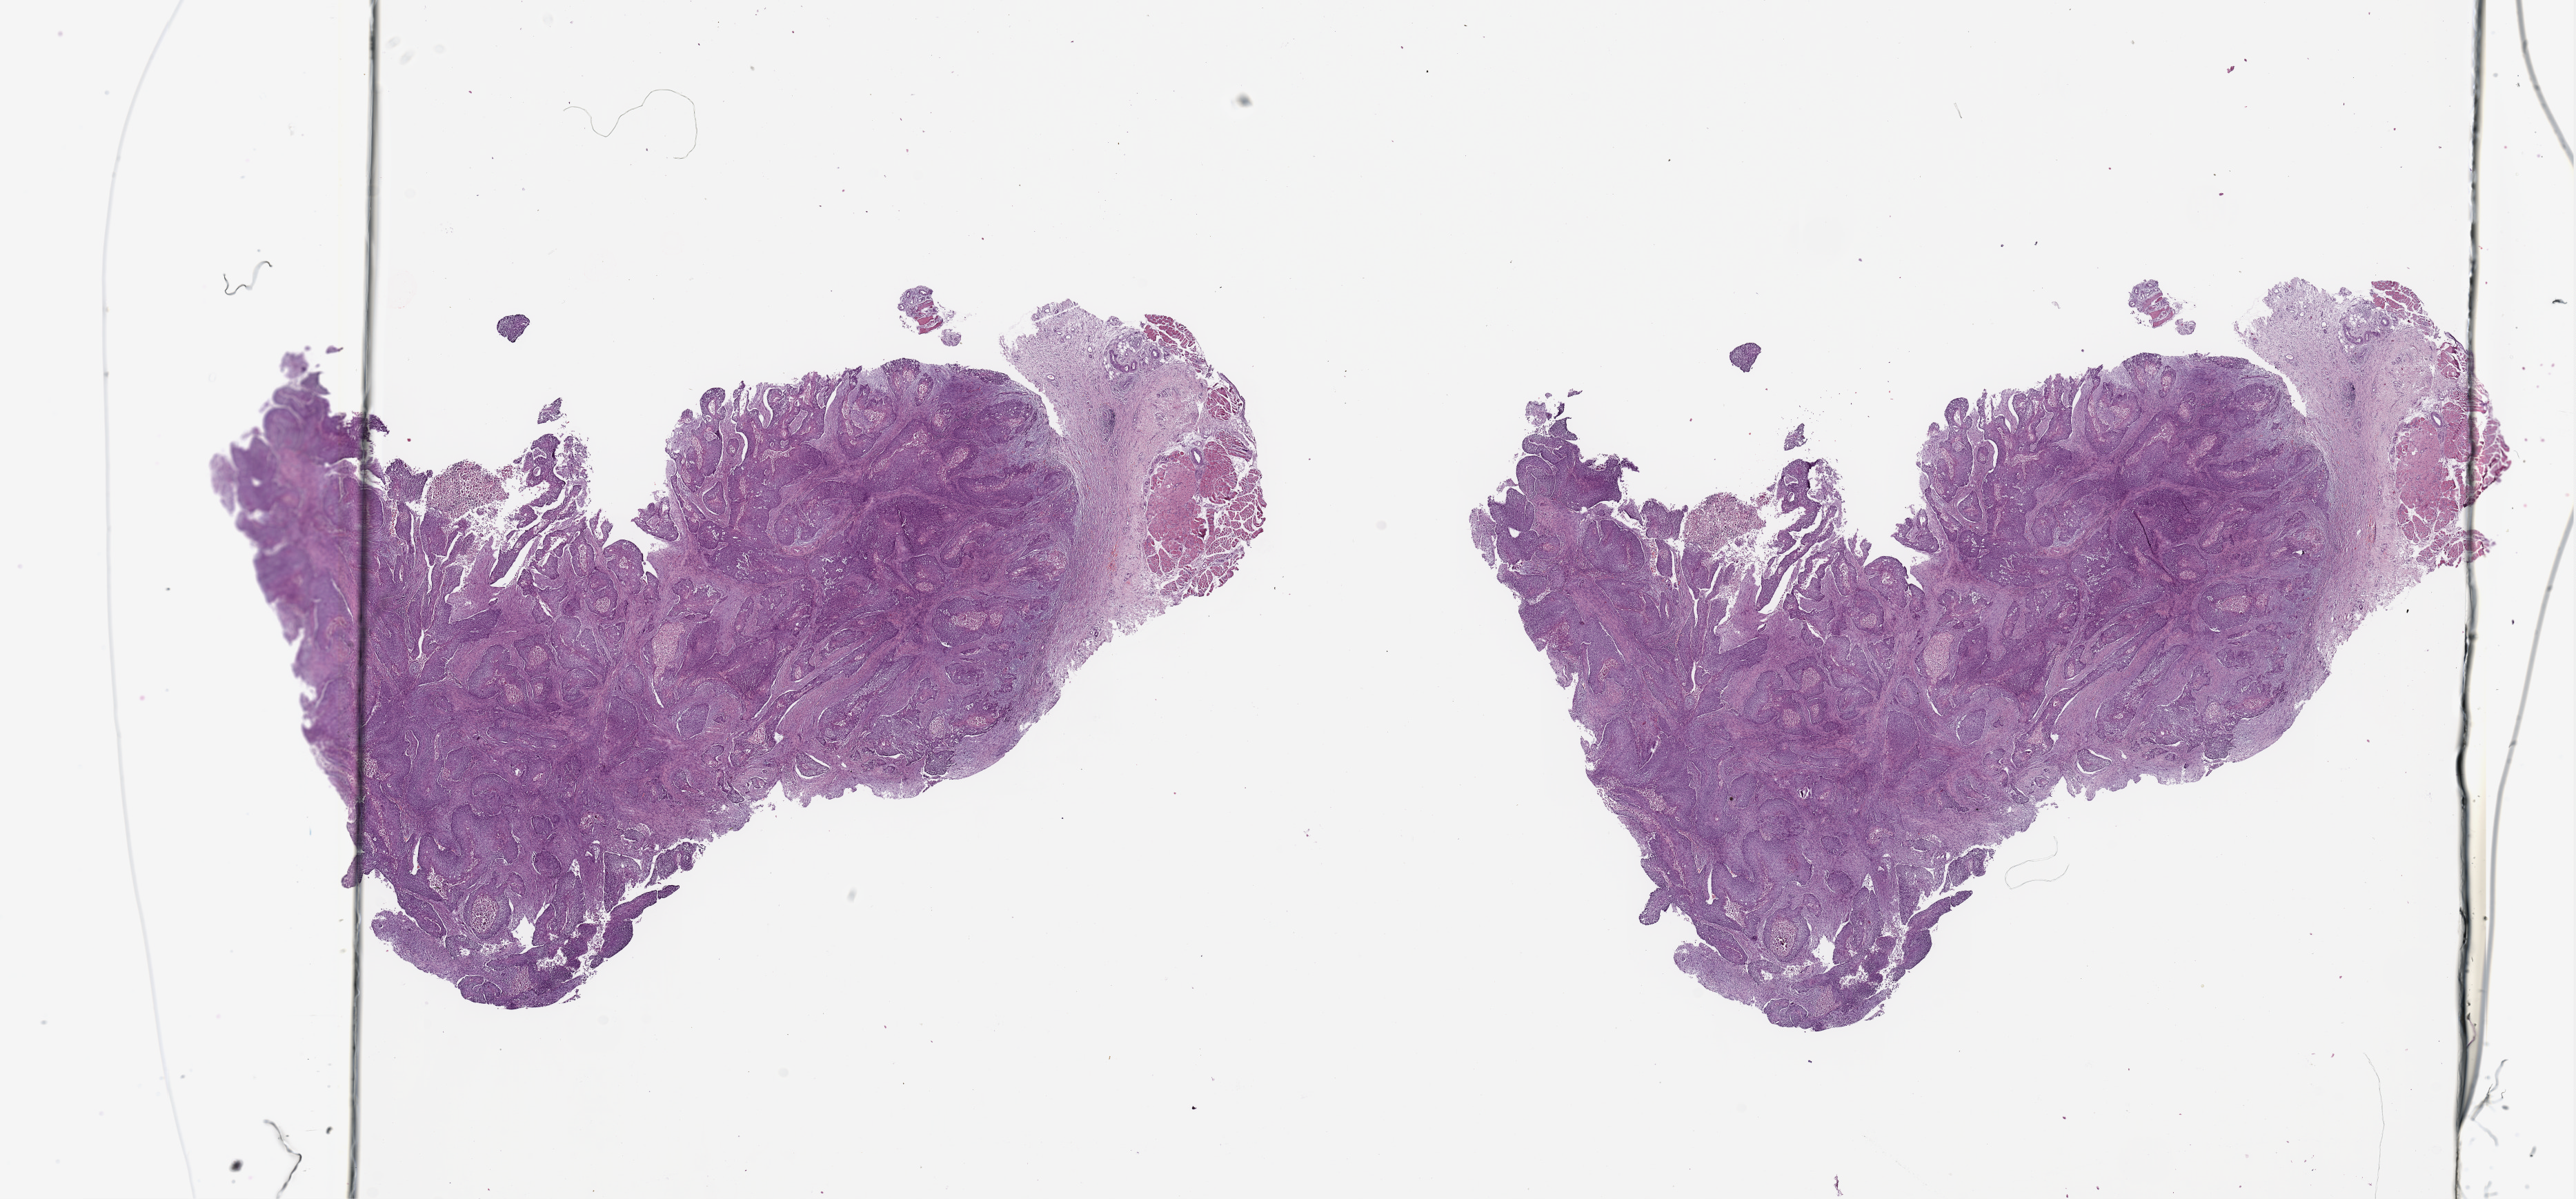
Whole-slide histology image, H&E, low-resolution overview of the scanned area, about 29.5 x 13.7 mm (from a 20x scan); head and neck, tissue type not recorded. 53-year-old male patient.
Patient diagnosis: Squamous cell carcinoma, NOS (oropharynx, NOS).